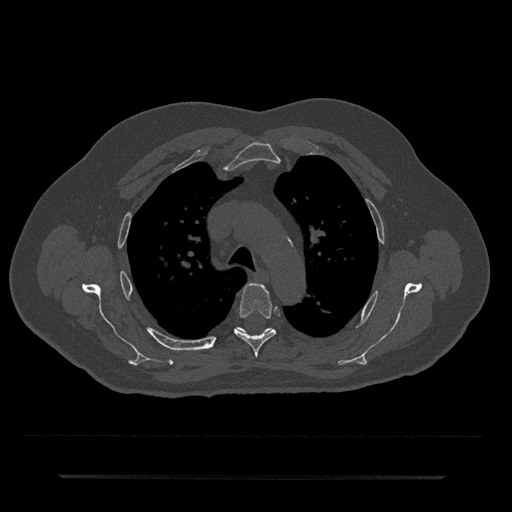
CT including the spine, one axial slice. Position 521 of 797 along the scan axis. Reconstruction kernel Br40s/3. 120 kVp. Bone window (W 1800 / L 400 HU). 512 × 512 image matrix, field of view 437 × 437 mm. Male patient, age 69 years. From the clinical record (not read from this slice): primary cancer: prostate.
Outlined on this slice (semi-automatically segmented with operator editing):
- T4 vertebra: bounding box <234,283,276,358> (left, top, right, bottom; pixels)
- T5 vertebra: <236,327,273,334>